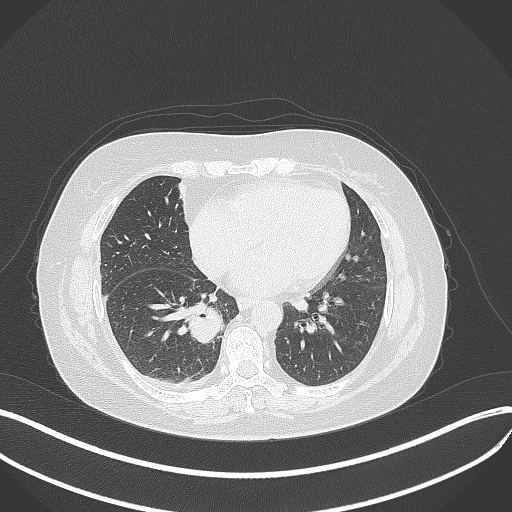
Chest CT, one axial slice. Position 139 of 381 along the scan axis. Reconstruction kernel B70f. 120 kVp. Lung window (W 1500 / L -600 HU). 512 × 512 image matrix, field of view 400 × 400 mm. Female patient, age 56 years. From the clinical record (not read from this slice): clinical TNM (as recorded): T2b N1 M0.
Annotated regions visible in this slice (bounding box drawn by a radiologist):
- lung tumour (recorded histology: small cell carcinoma): bounding box [x1, y1, x2, y2] px = [184, 306, 228, 346]